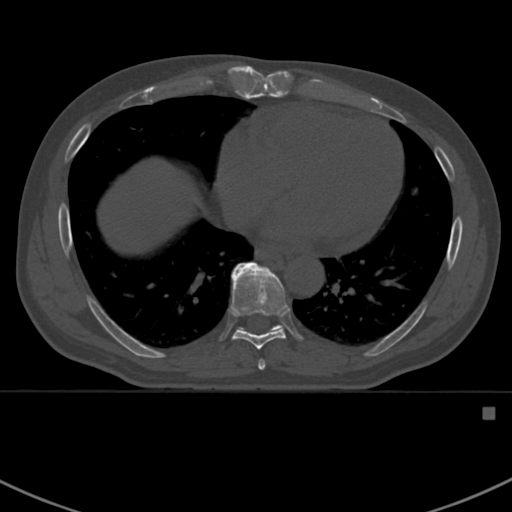
CT including the spine, one axial slice; slice 397 of 412 in the series (ordered by position); 120 kVp; bone window (W 1800 / L 400 HU); 1.5 mm slice thickness; 512 × 512 image matrix. Patient: male, 59 years. From the clinical record (not read from this slice): primary cancer: prostate.
Outlined on this slice (semi-automatically segmented with operator editing):
- T7 vertebra: bounding box (x1, y1, x2, y2) in pixels: (258, 359, 265, 370)
- T8 vertebra: (229, 265, 286, 350)
- T9 vertebra: (231, 262, 286, 332)